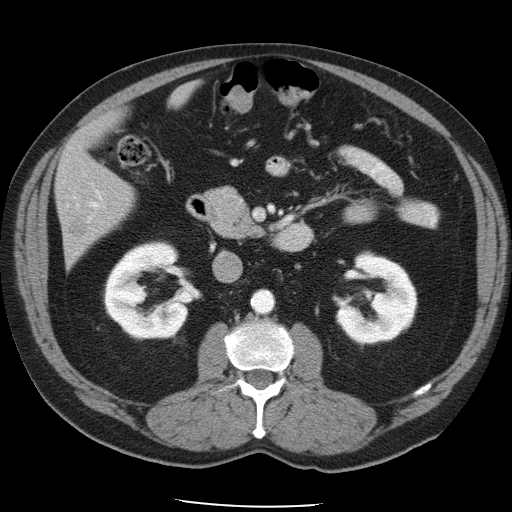
Contrast-enhanced abdominal CT, one axial slice; slice 20 of 49 in the series (ordered by position); reconstruction kernel STANDARD; intravenous contrast given; soft-tissue window (W 400 / L 40 HU); 5 mm slice thickness; 512 × 512 image matrix, field of view 395 × 395 mm. Male patient, age 68 years. From the clinical record (not read from this slice): diagnosis: colorectal cancer liver metastases, imaged before liver resection; multiple liver metastases: yes; largest metastasis: 1.7 cm; chemotherapy before resection: yes.
Outlined on this slice (expert manual segmentation):
- hepatic veins: bounding box (x1, y1, x2, y2) in pixels: (77, 205, 79, 207)
- liver: (56, 88, 191, 263)
- planned liver remnant (the part of the liver to remain after resection): (60, 91, 186, 217)
- portal vein (with intrahepatic branches): (67, 191, 105, 223)
- liver metastasis: (69, 216, 89, 237)